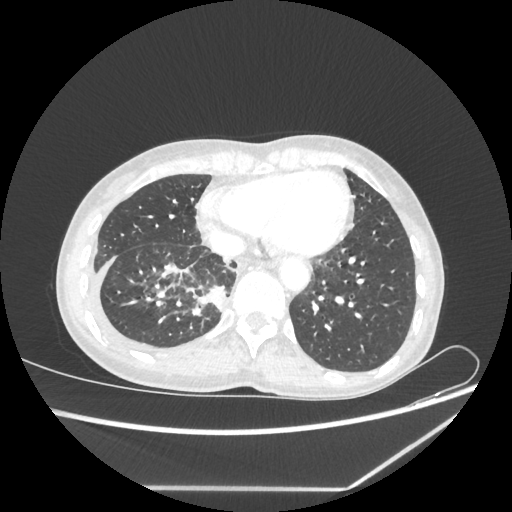
Chest CT, one axial slice; lung window (W 1500 / L -600 HU); 1.25 mm slice thickness; 512 × 512 image matrix, field of view 364 × 364 mm. Female patient, age 59 years. Case-level facts recorded for this patient, not image findings: clinical TNM (as recorded): T1c N1 M1.
Structures marked on this image (bounding box drawn by a radiologist):
- lung tumour (recorded histology: adenocarcinoma): box from (x=205, y=281) to (x=228, y=314) px